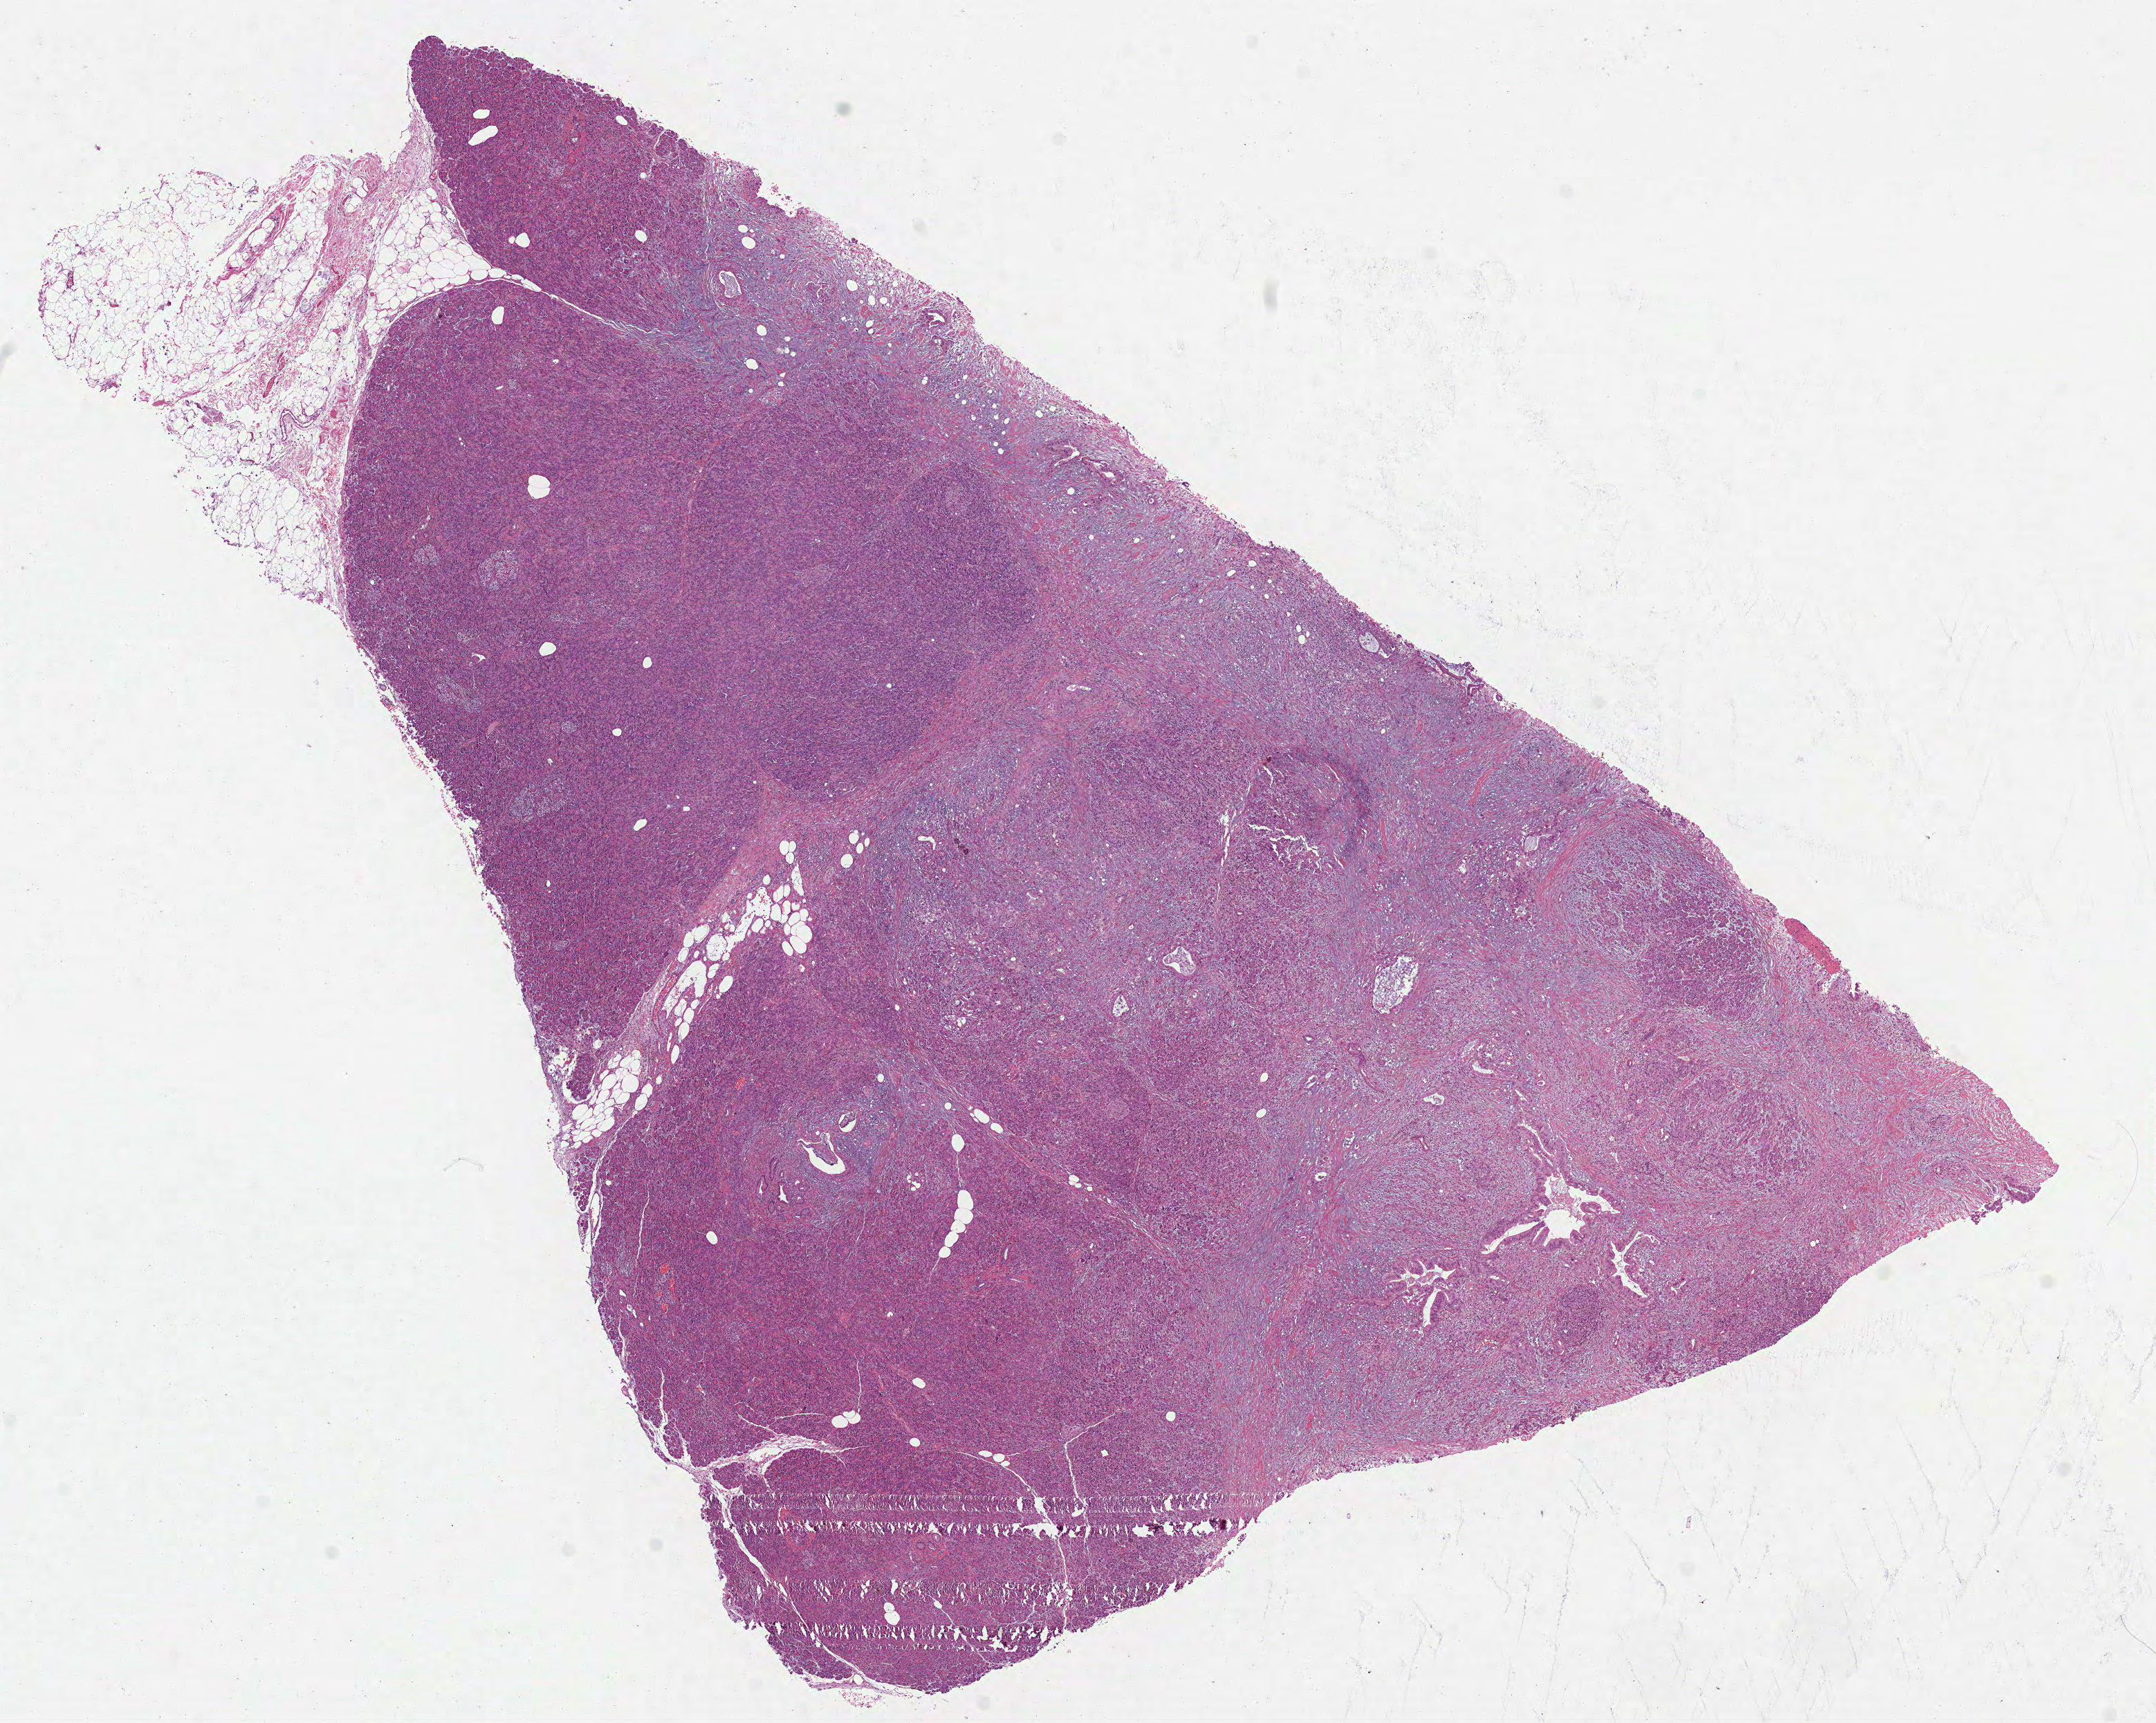
H&E-stained whole-slide image, whole scanned area (about 12.6 x 10.0 mm, slide scanned at 40x) shown as a low-resolution overview; FFPE section; sample: primary tumour, pancreas. Male, age 72 years at initial diagnosis. Histologic grade: G3 (poorly differentiated).
- AJCC pathologic stage: IIB (7th edition)
- pathologic diagnosis: Adenocarcinoma, NOS
- lymph nodes positive (case pathology): 2 of 4 examined
- TNM: T3 N1 MX